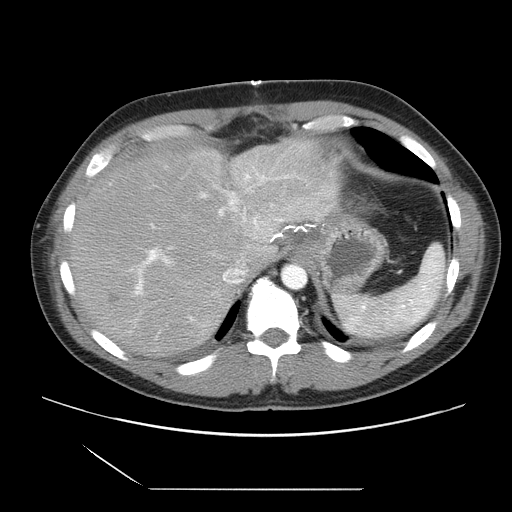
Contrast-enhanced abdominal CT, one axial slice; position 23 of 39 along the scan axis; 120 kVp; intravenous contrast given; soft-tissue window (W 400 / L 40 HU); 5 mm slice thickness; 512 × 512 image matrix, field of view 395 × 395 mm. Male patient, age 39 years. Case-level facts recorded for this patient, not image findings: diagnosis: colorectal cancer liver metastases, imaged before liver resection; multiple liver metastases: yes; largest metastasis: 1.3 cm; disease in both lobes: no.
Annotated regions visible in this slice (outlined manually by an expert reader):
- hepatic veins: bounding box (x1, y1, x2, y2) in pixels: (203, 260, 247, 304)
- liver: (73, 140, 341, 357)
- planned liver remnant (the part of the liver to remain after resection): (116, 141, 341, 267)
- portal vein (with intrahepatic branches): (109, 166, 290, 322)
- liver metastasis: (108, 293, 120, 304)